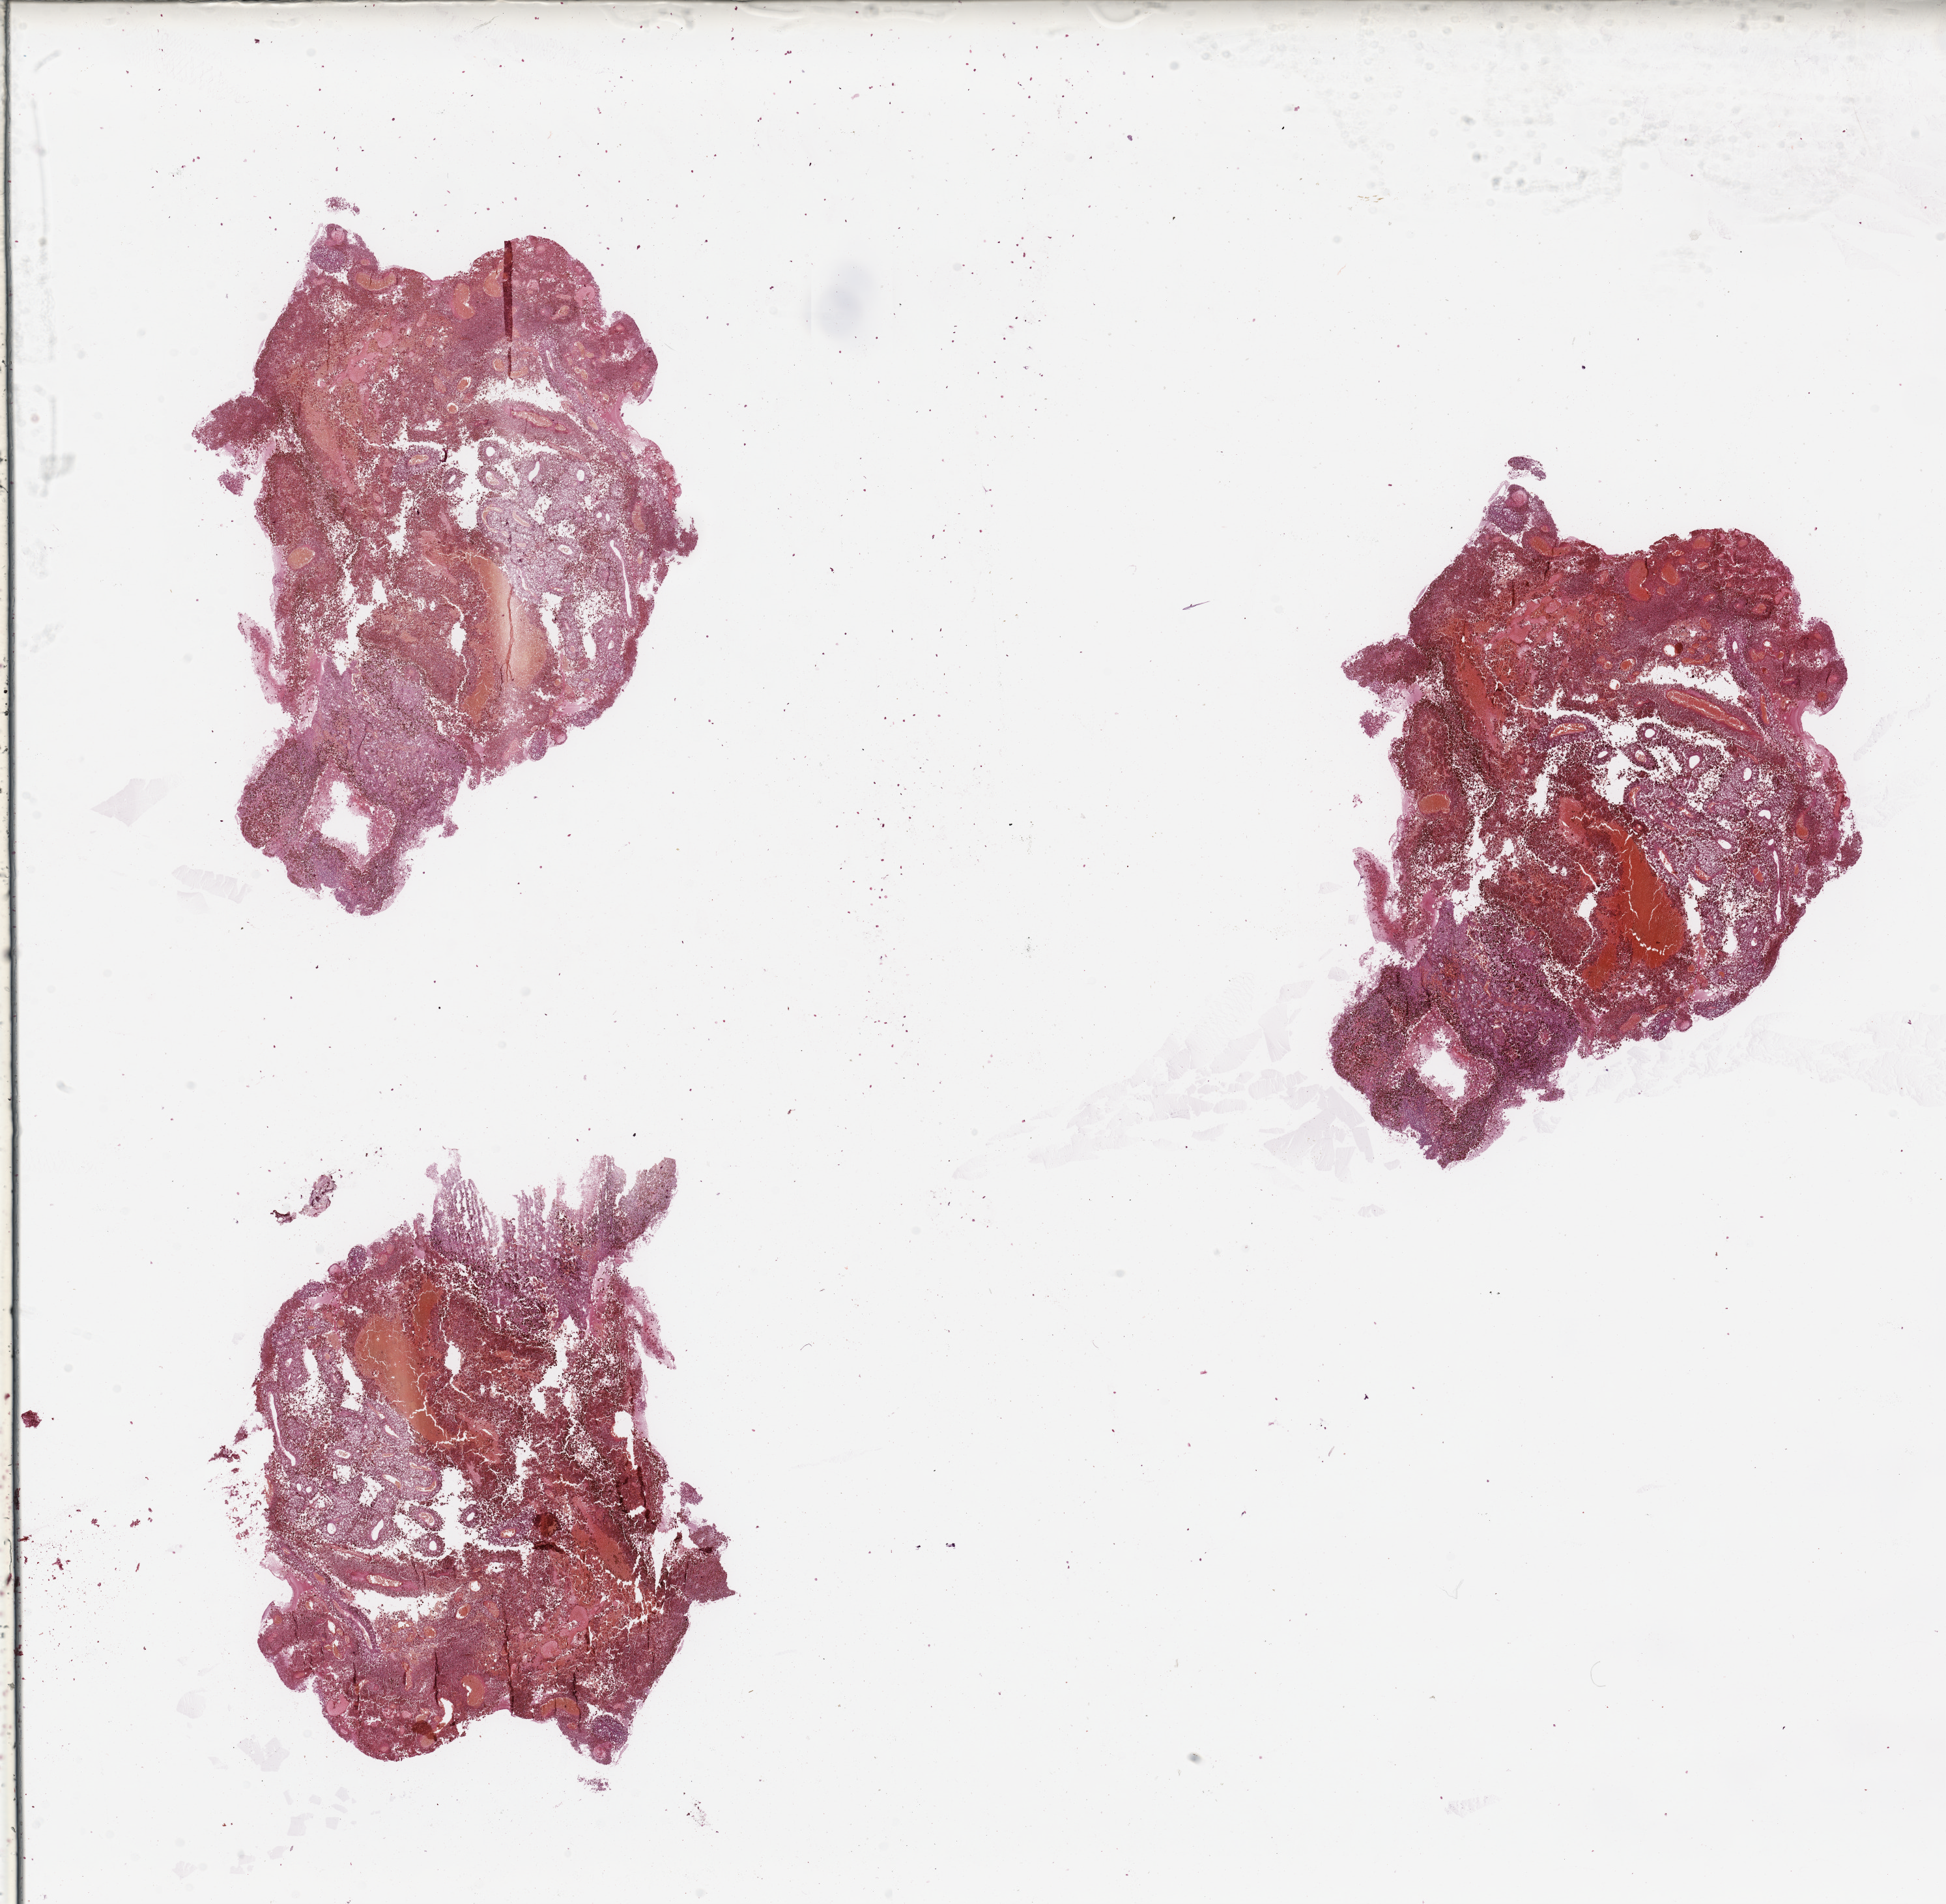
H&E whole-slide image, whole scanned area (about 23.6 x 23.1 mm) shown as a low-resolution overview, tumour tissue sample, sampled site: skin. Patient: female, age 67 years. Slide review estimates, as recorded: tumour nuclei 90%, necrosis 20%.
• this section: metastatic tumour tissue
• patient diagnosis: Malignant melanoma, NOS
• primary tumour site (as recorded): extremities